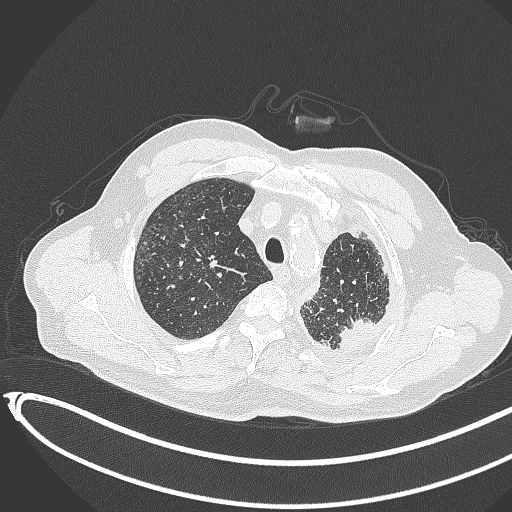
Chest CT, one axial slice. Reconstruction kernel B70f. 120 kVp. Lung window (W 1500 / L -600 HU). 512 × 512 image matrix, field of view 400 × 400 mm. Patient: male, 78 years. From the clinical record (not read from this slice): clinical TNM (as recorded): T1c N0 M1.
Annotated regions visible in this slice (bounding box drawn by a radiologist):
- lung tumour (recorded histology: adenocarcinoma): bounding box [x1, y1, x2, y2] px = [330, 308, 378, 356]